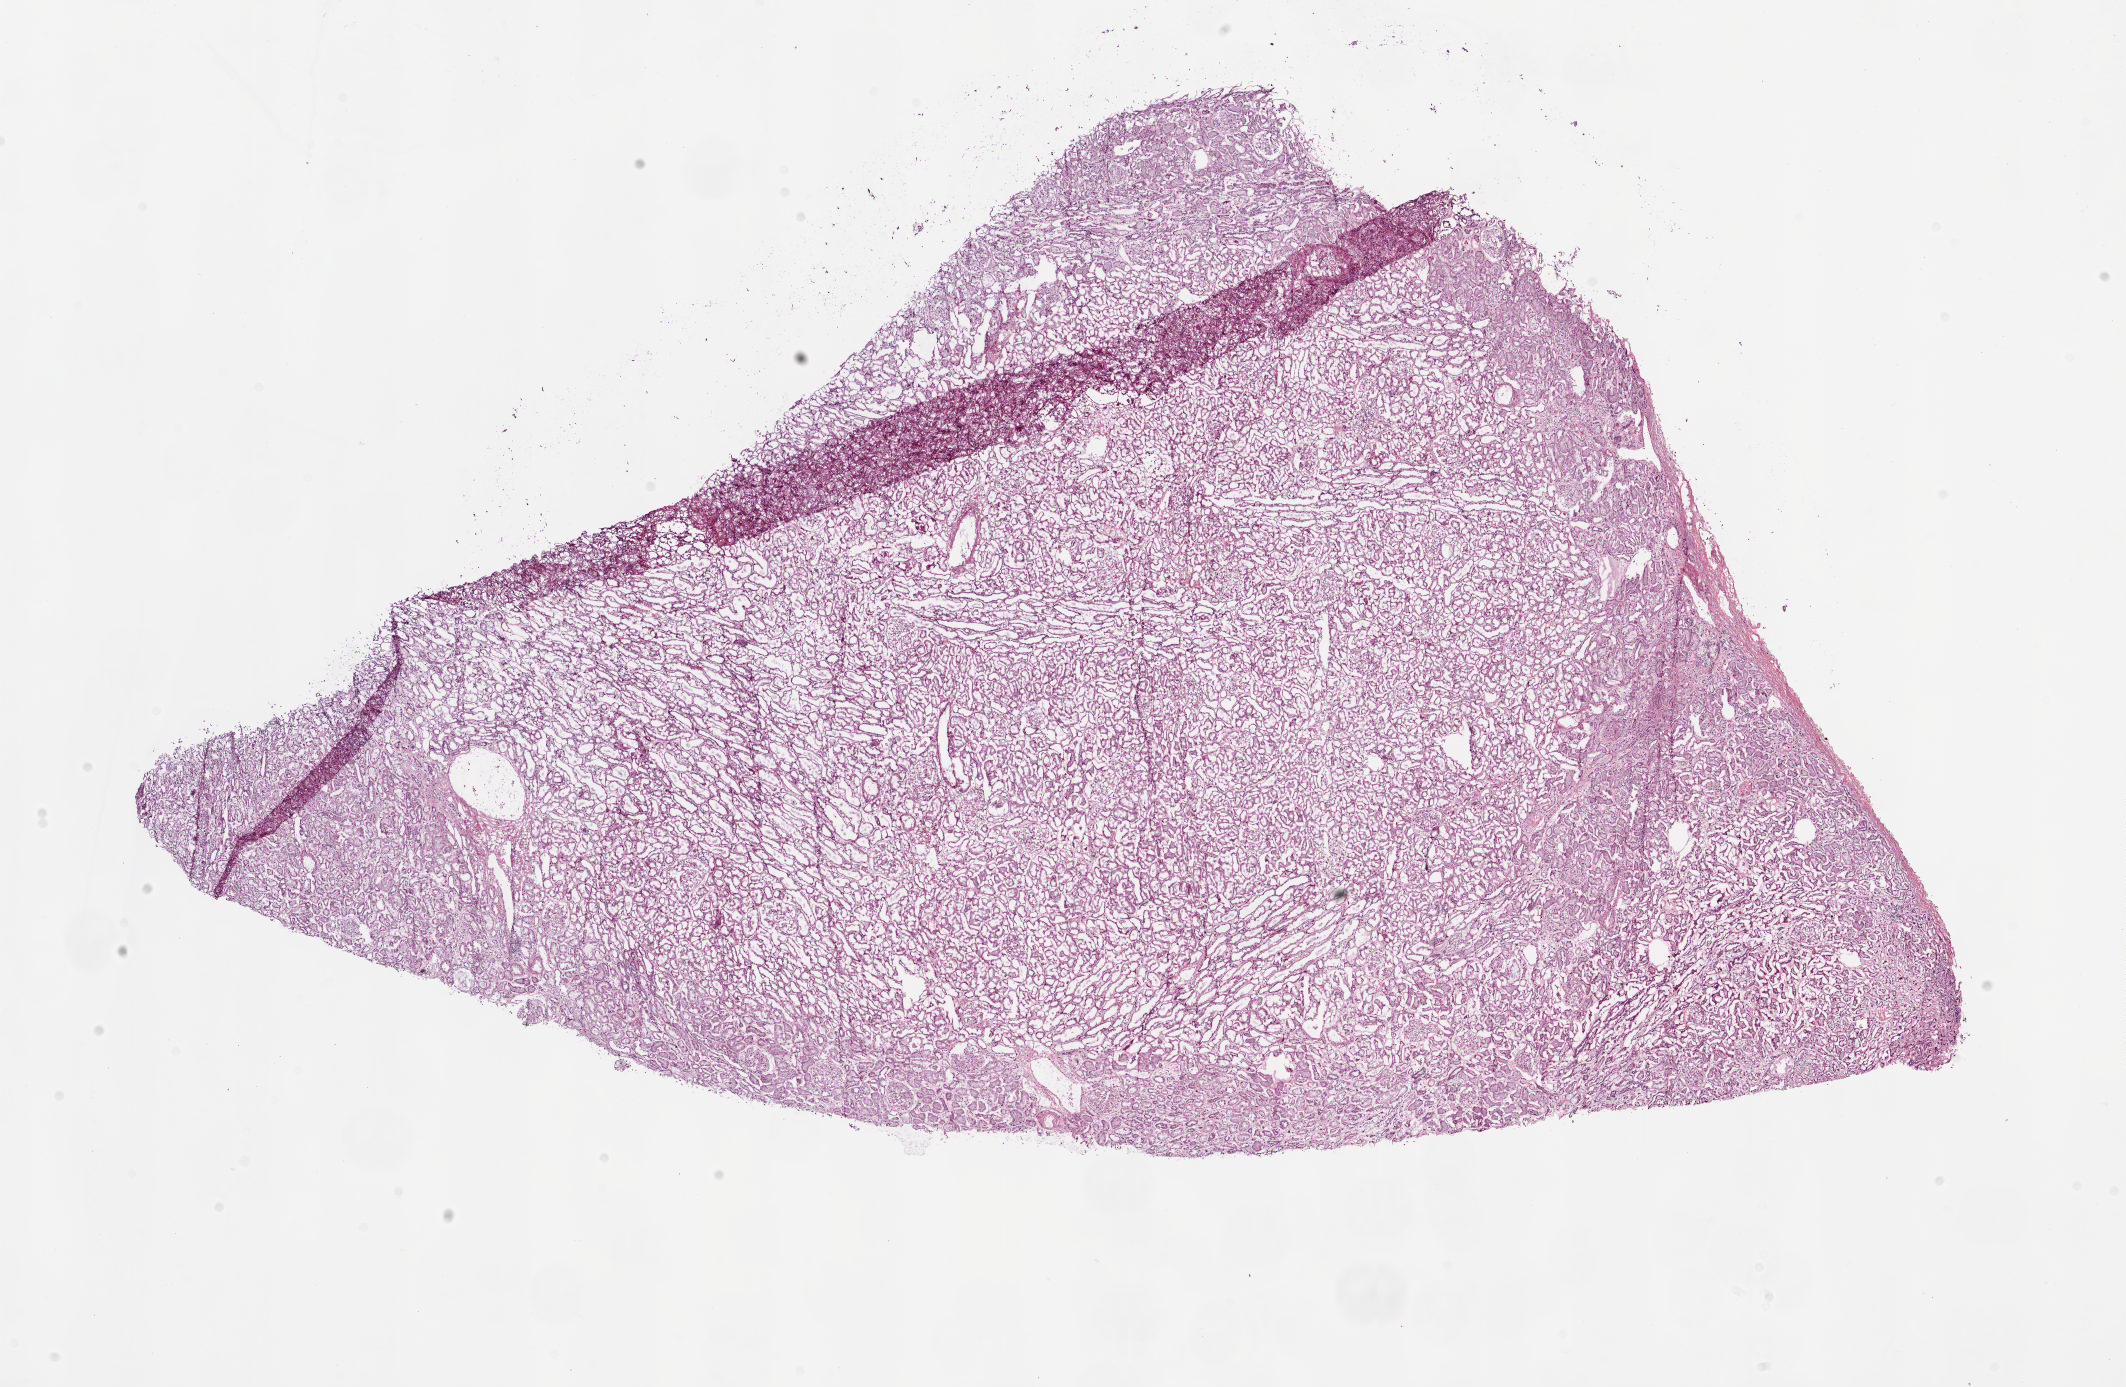
H&E whole-slide image, a low-resolution overview of the entire scanned area, about 16.9 x 11.0 mm (from a 20x scan), frozen section from the bottom of the tissue portion, kidney, solid tissue normal (non-tumour tissue) sample. Patient: male, age at initial diagnosis 74 years.
This section: solid tissue normal sample (biorepository sample class). Patient diagnosis: Clear cell adenocarcinoma, NOS.